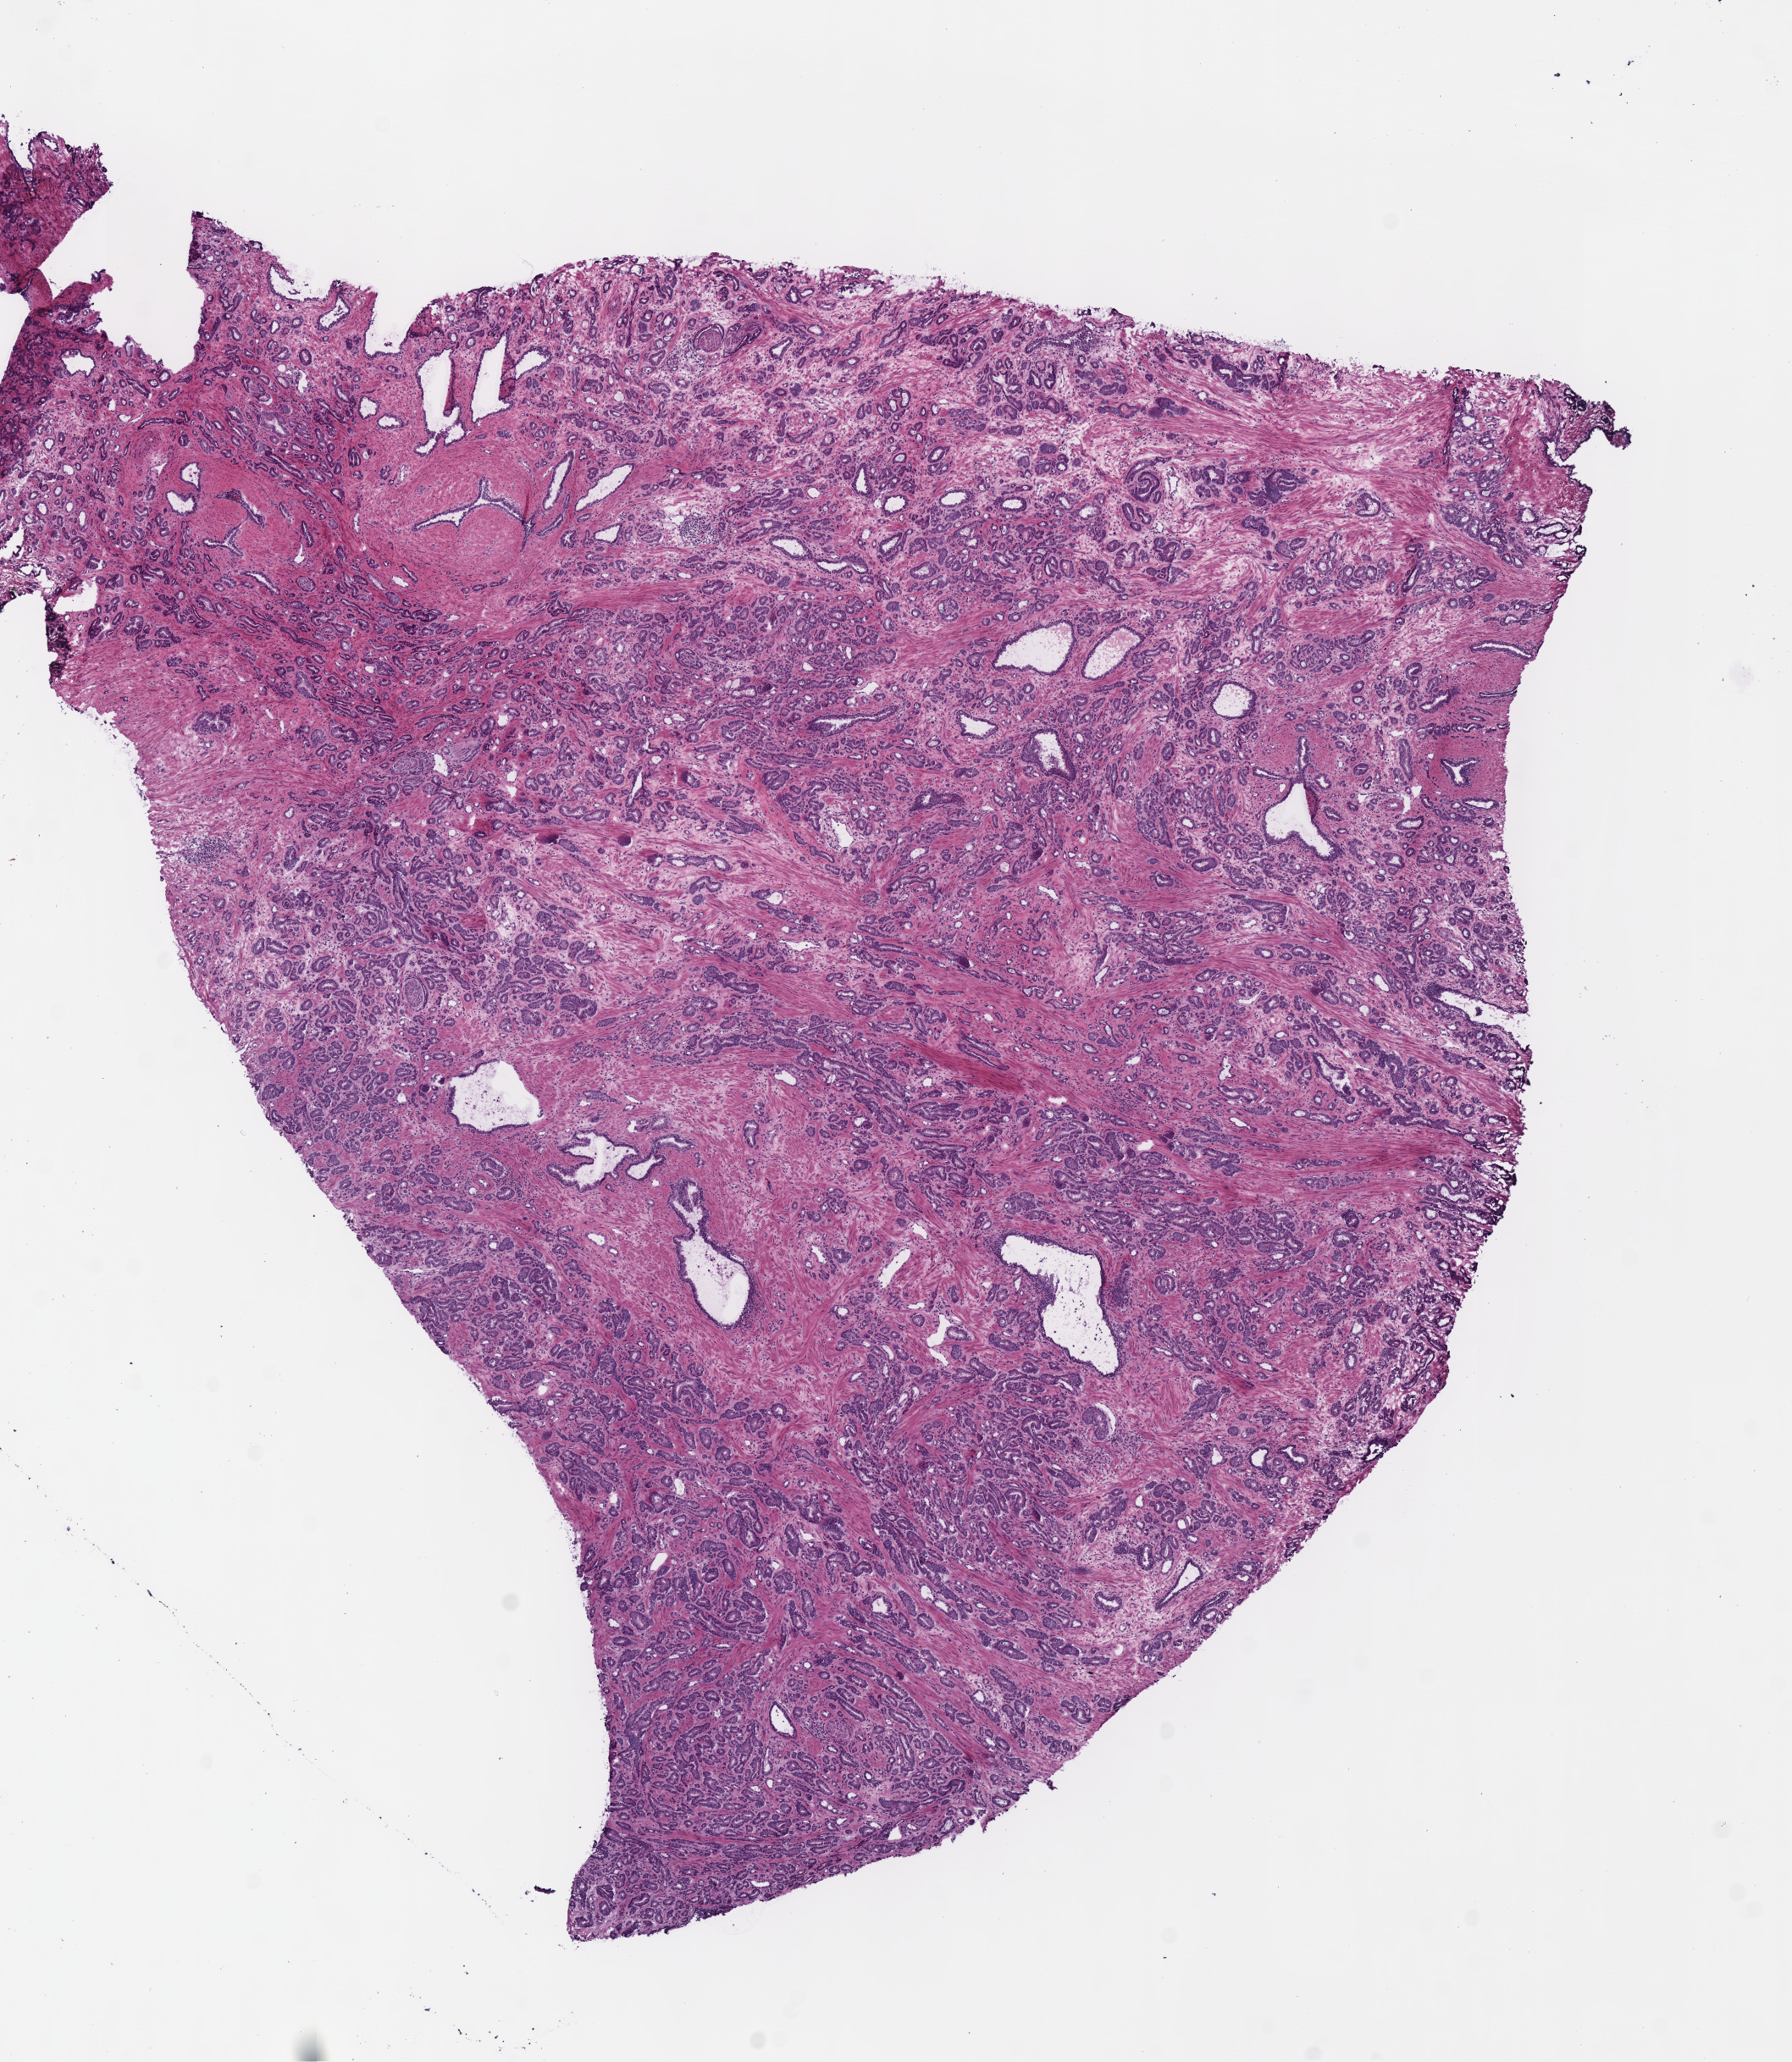
Hematoxylin and eosin (H&E) stained whole-slide image — a low-resolution overview of the entire scanned area, about 8.3 x 9.6 mm; frozen section from the bottom of the tissue portion; prostate, primary tumour sample. Male patient; age at initial diagnosis 49 years. Gleason score: 7 (4+3). Pathologist review of this section (percent, as recorded): tumour cells 80%, tumour nuclei 80%, normal cells 5%, stromal cells 15%, necrosis 0%.
Pathologic diagnosis: Acinar cell carcinoma (prostate gland). Laterality: bilateral.